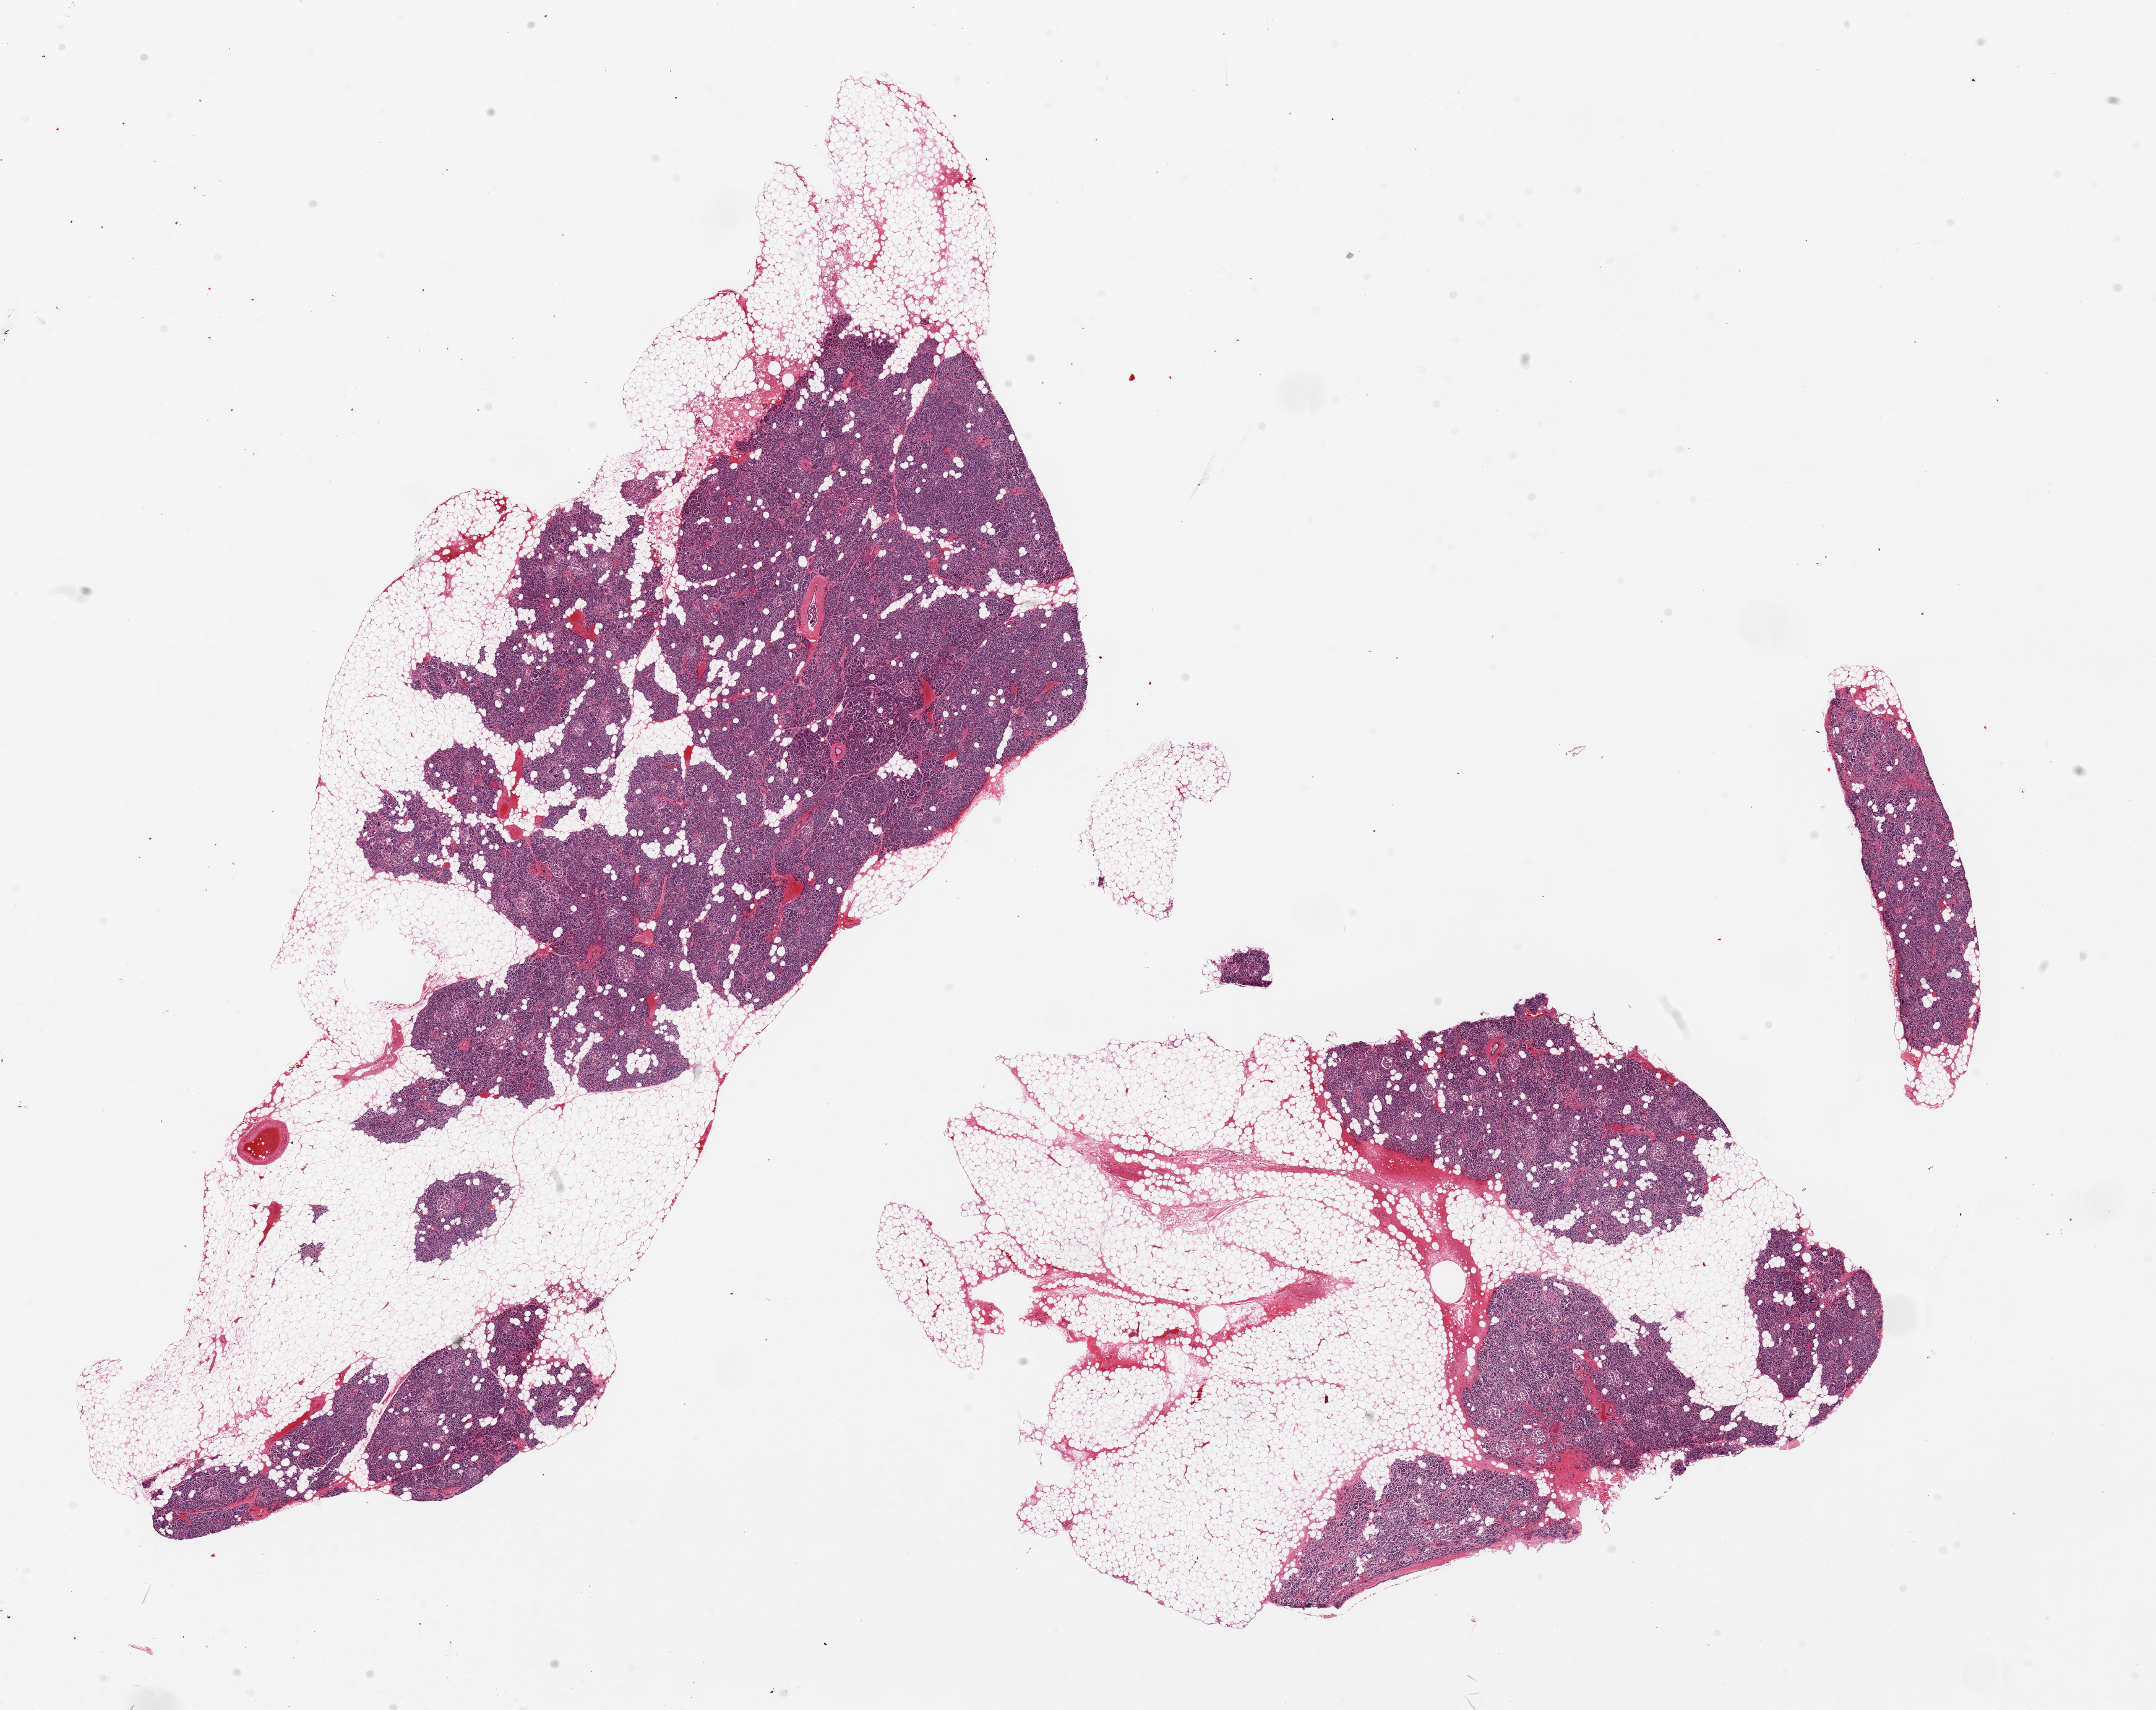
Whole-slide image, hematoxylin and eosin (H&E) stain, whole scanned area (about 27.6 x 21.9 mm) shown as a low-resolution overview. Donor: female.
Specimen: PAXgene-fixed, paraffin-embedded tissue; section of pancreas (target tissue); donor tissue sample.